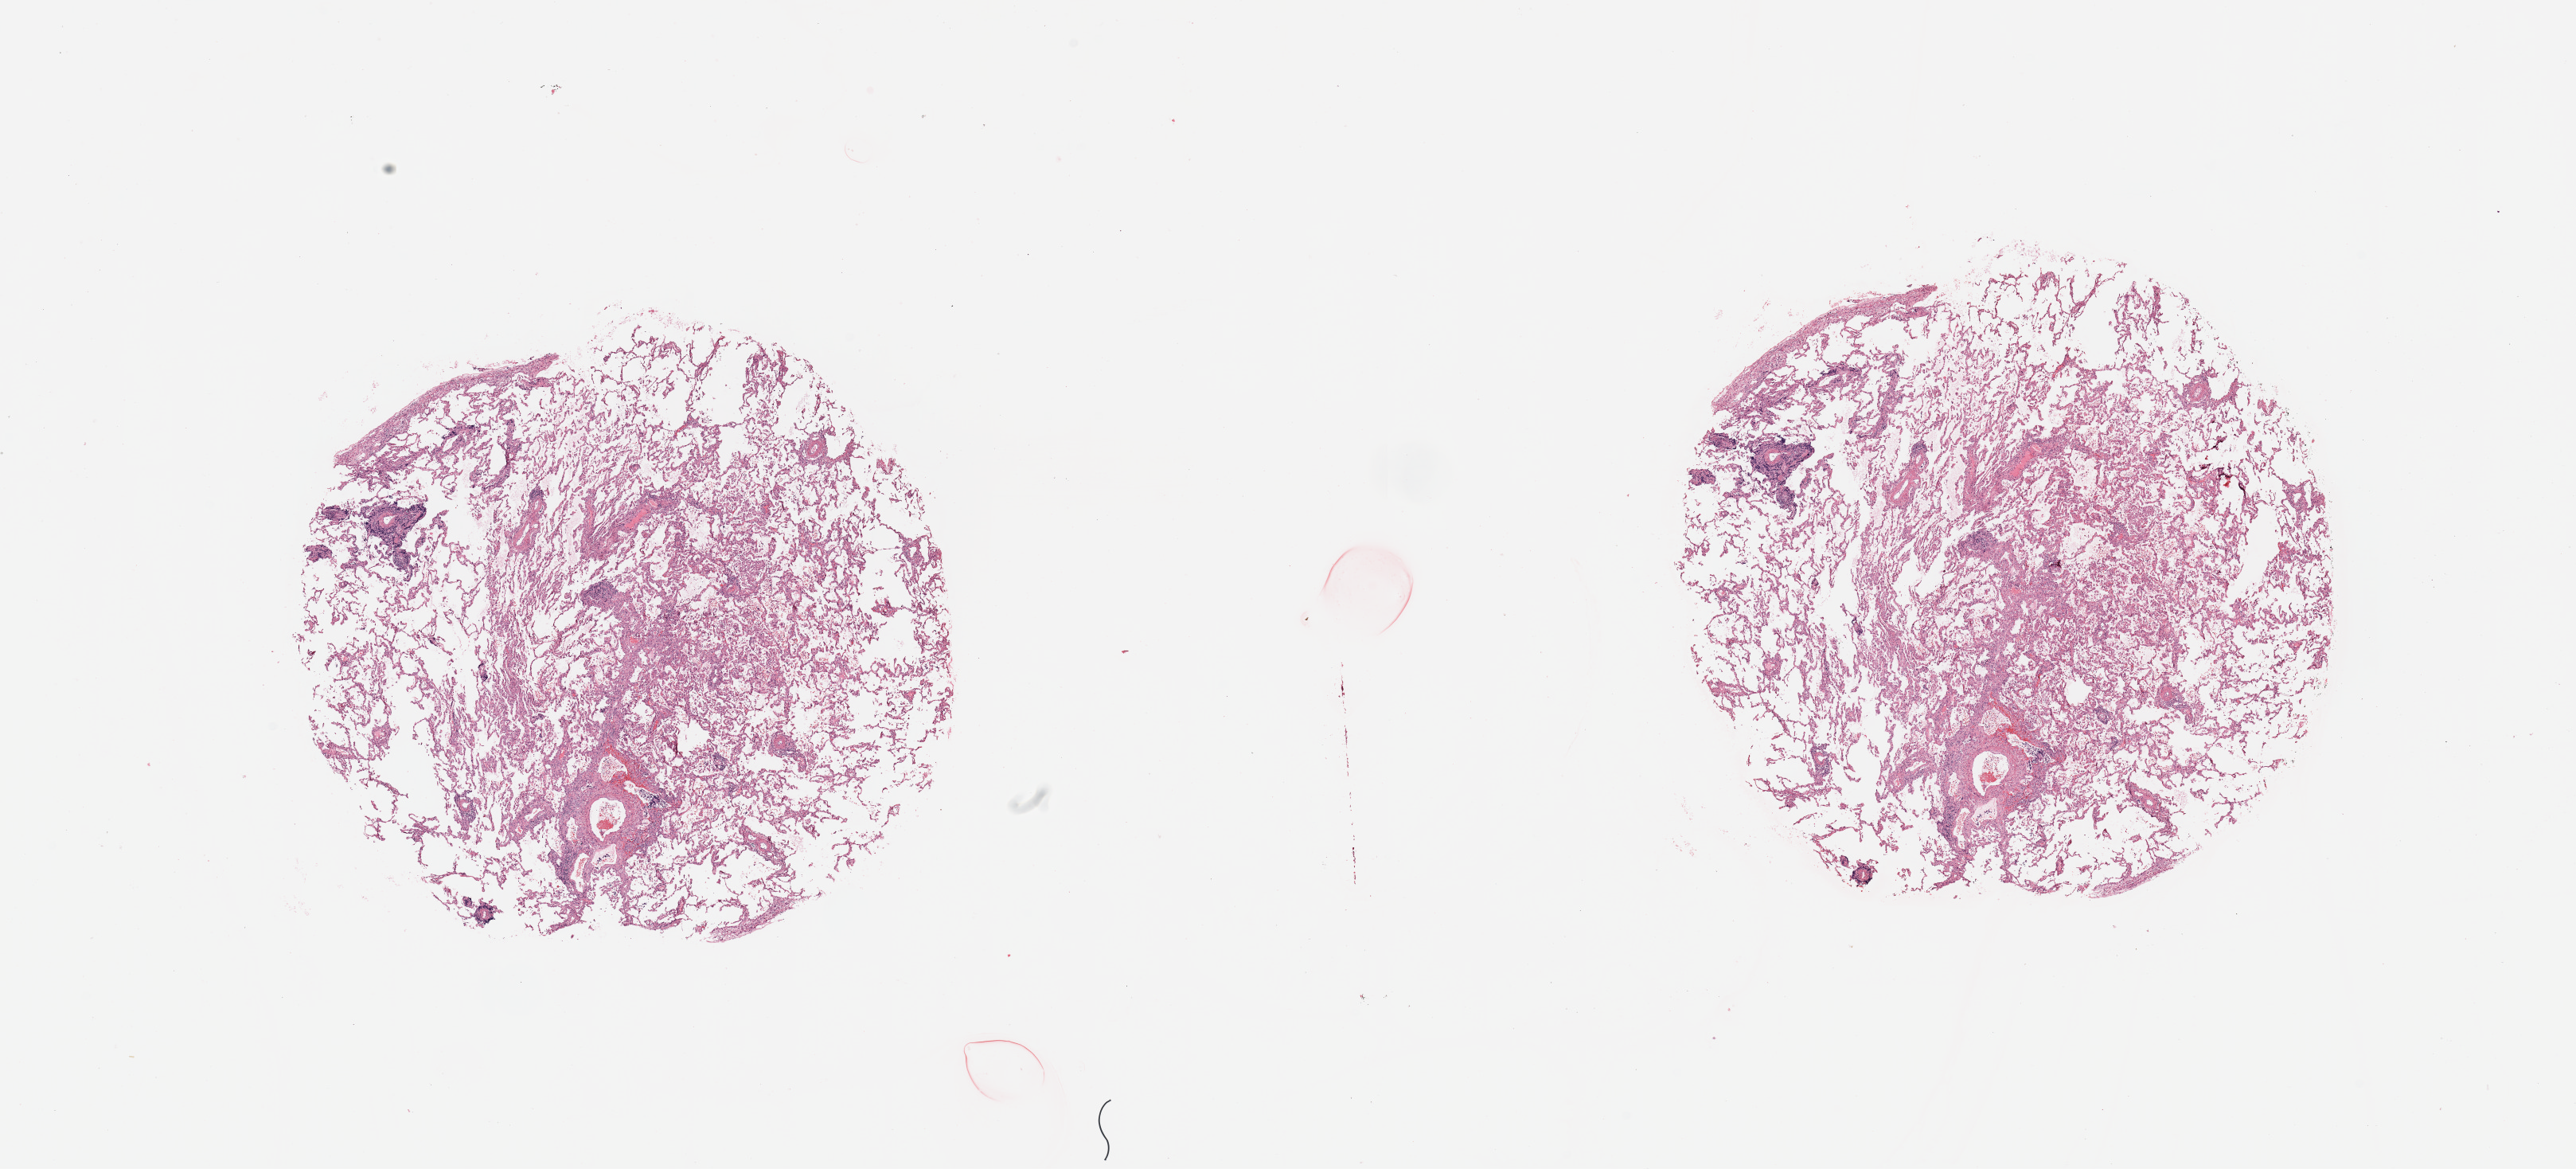
H&E whole-slide image, shown as a low-resolution overview of the whole scanned area (about 25.6 x 11.6 mm), normal (non-tumour) tissue sample, lung. Patient: male, age 63 years.
- this section: normal (non-tumour) tissue from the same patient
- patient diagnosis: Adenocarcinoma, NOS